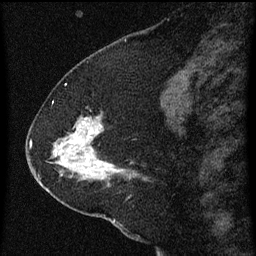
Breast MRI (dynamic contrast-enhanced), one sagittal slice; position 24 of 60 along the scan axis; dynamic contrast-enhanced series, image 2 of 3 at this slice position (ordered by acquisition); 1.5 T; TE 4.2 ms, TR 8 ms; 256 × 256 image matrix, field of view 180 × 180 mm. Patient: female, 47 years.
Structures marked on this image (semi-automatic segmentation, software-assisted and operator-edited):
- analysis volume of interest (the breast-tissue region the enhancement analysis was run in; not a lesion): bounding box (x1, y1, x2, y2) in pixels: (36, 100, 154, 213)
- tumour enhancement mask (voxels above the 70 % enhancement threshold inside the analysis volume of interest): (53, 118, 131, 179)